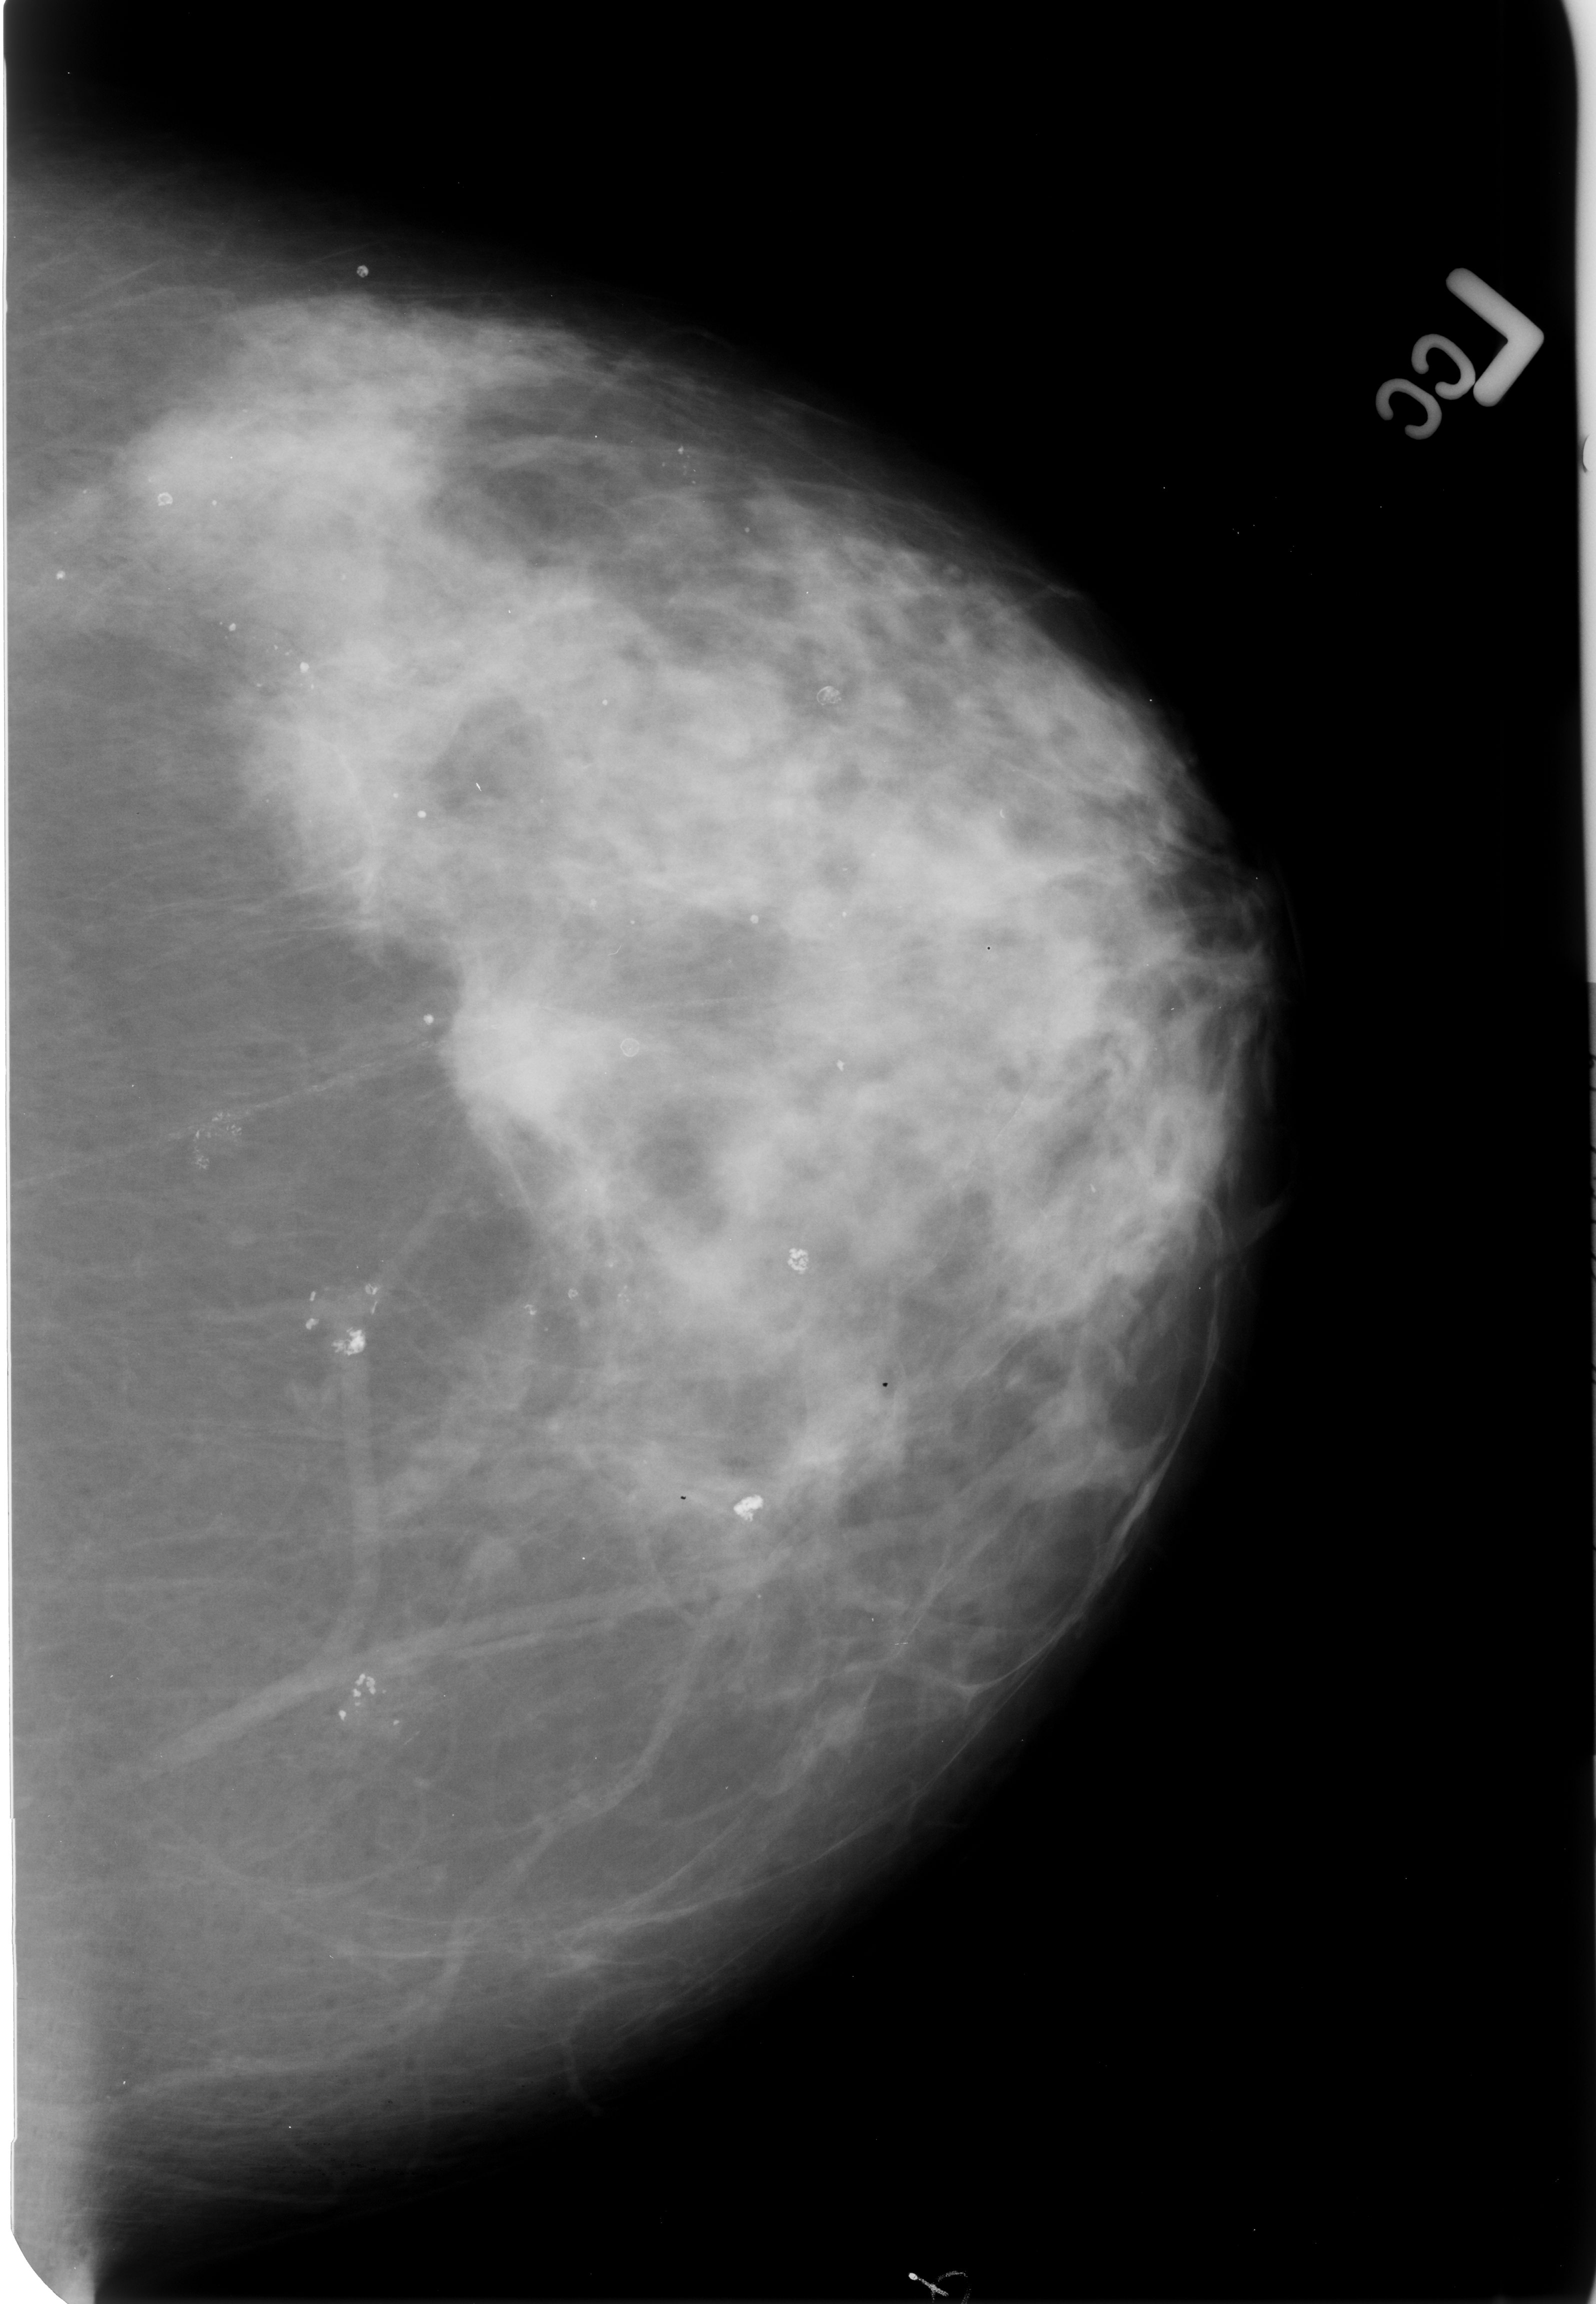
Mammogram (digitized film); left breast; CC view; 1596 × 2304 image matrix.
Expert-marked regions of interest on this image (one box per marked abnormality):
- mass, shape irregular / architectural distortion, margins ill defined / spiculated; BI-RADS assessment category 4; subtlety rating 4 on a 1 (subtle) to 5 (obvious) scale; pathology result (as recorded, not read from the image): malignant: box from (x=449, y=1009) to (x=580, y=1144) px